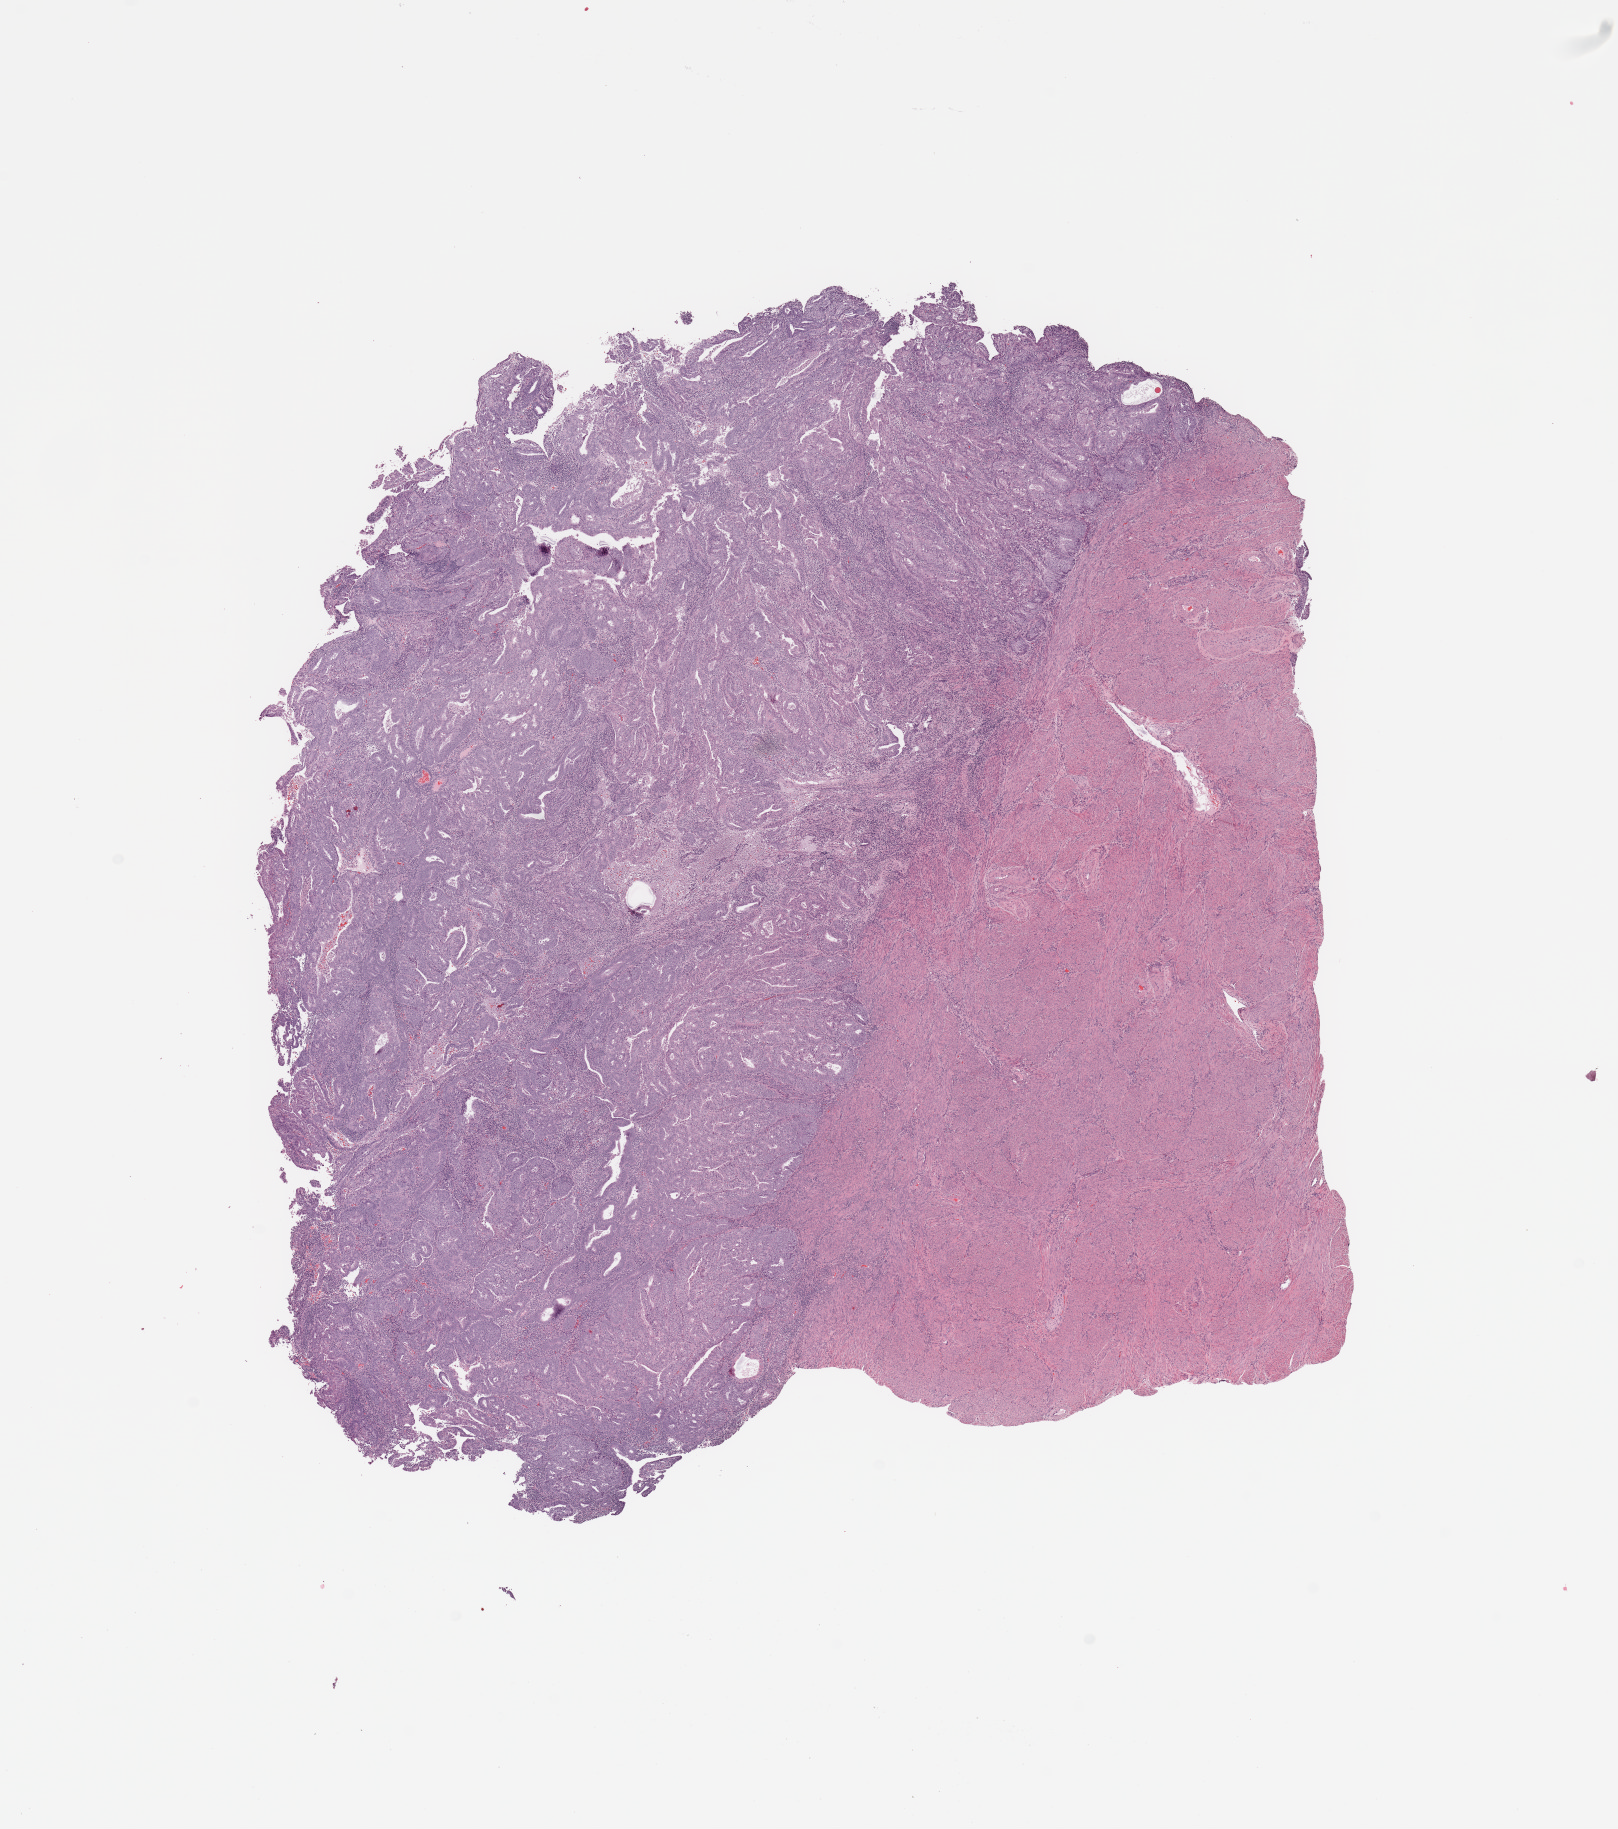
Whole-slide histology image, H&E, whole scanned area (about 12.8 x 14.5 mm, acquisition: 20x scan) shown as a low-resolution overview. Tumour tissue sample, sampled site: uterus. 59-year-old female patient. Histologic grade: G1 (well differentiated). Composition of this section per pathologist review: tumour nuclei 80%, necrosis 1%.
* AJCC pathologic stage: I
* primary tumour site (as recorded): anterior endometrium
* diagnosis: Endometrioid adenocarcinoma, NOS